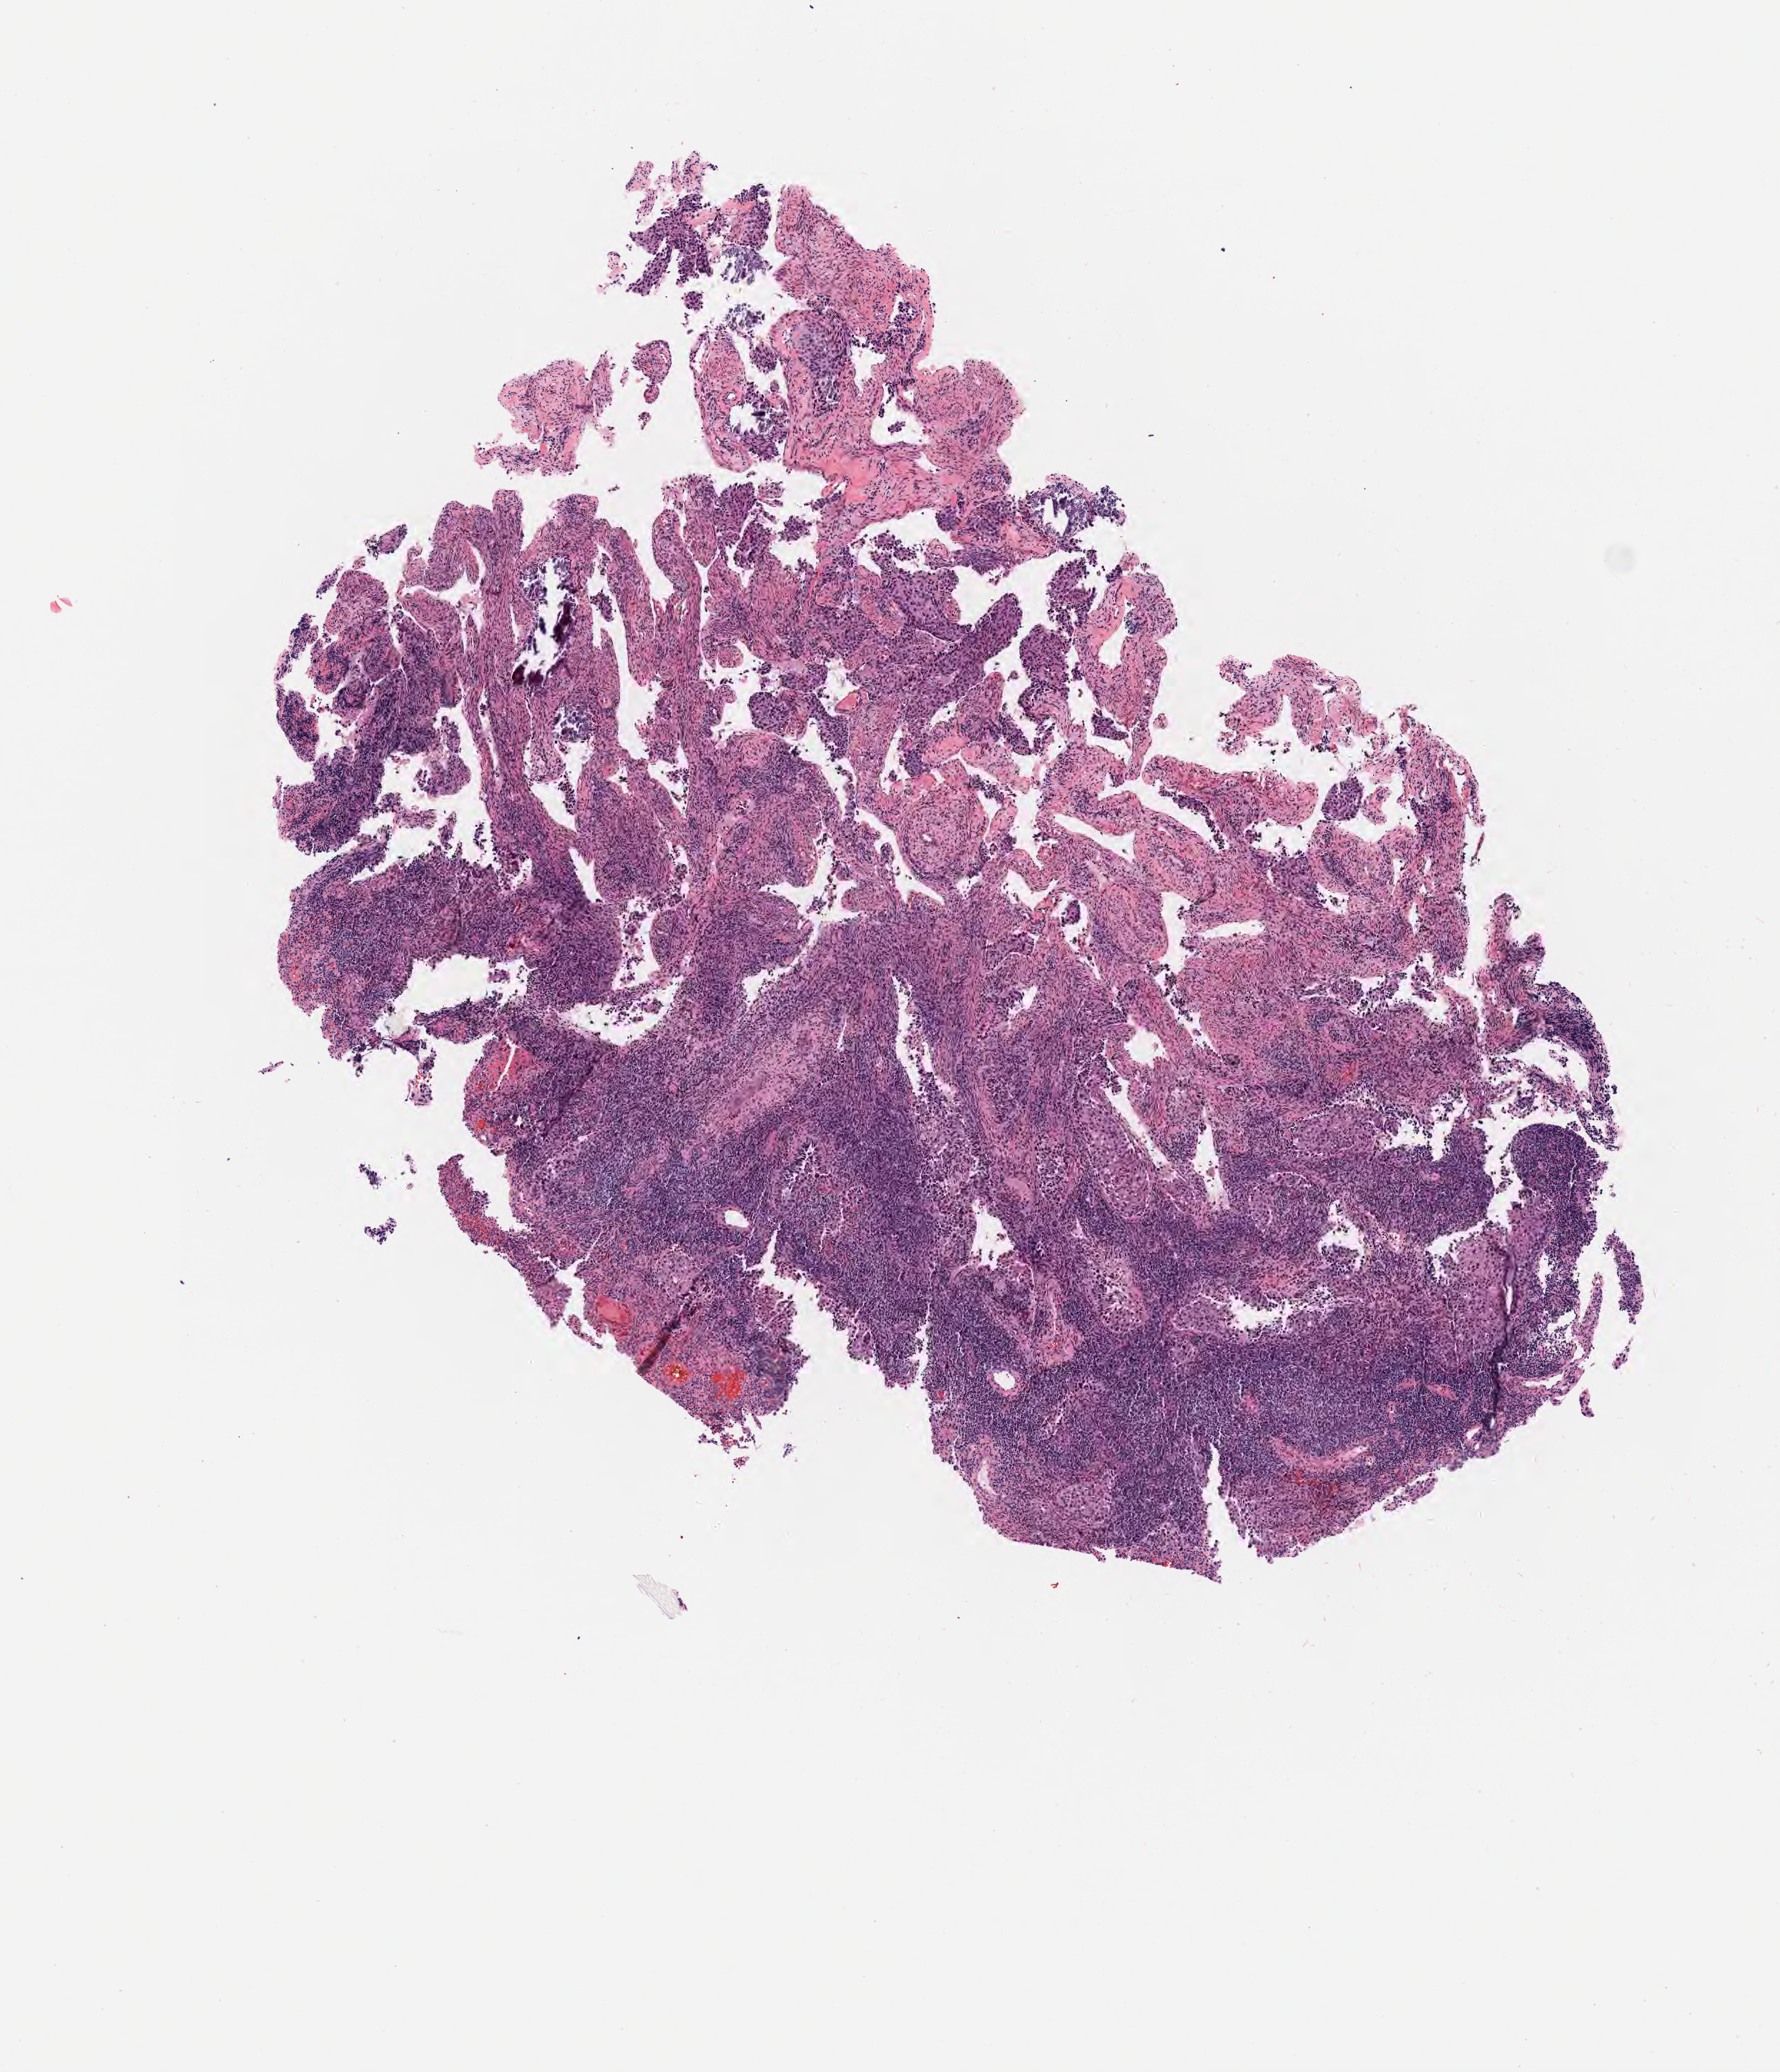
Whole-slide image, hematoxylin and eosin (H&E) stain, whole scanned area (about 5.0 x 5.9 mm) shown as a low-resolution overview. Specimen: tumor tissue. Site: cervix. Patient: female, age 48 years.
Histologic diagnosis: Squamous cell carcinoma, large cell, nonkeratinizing, NOS.